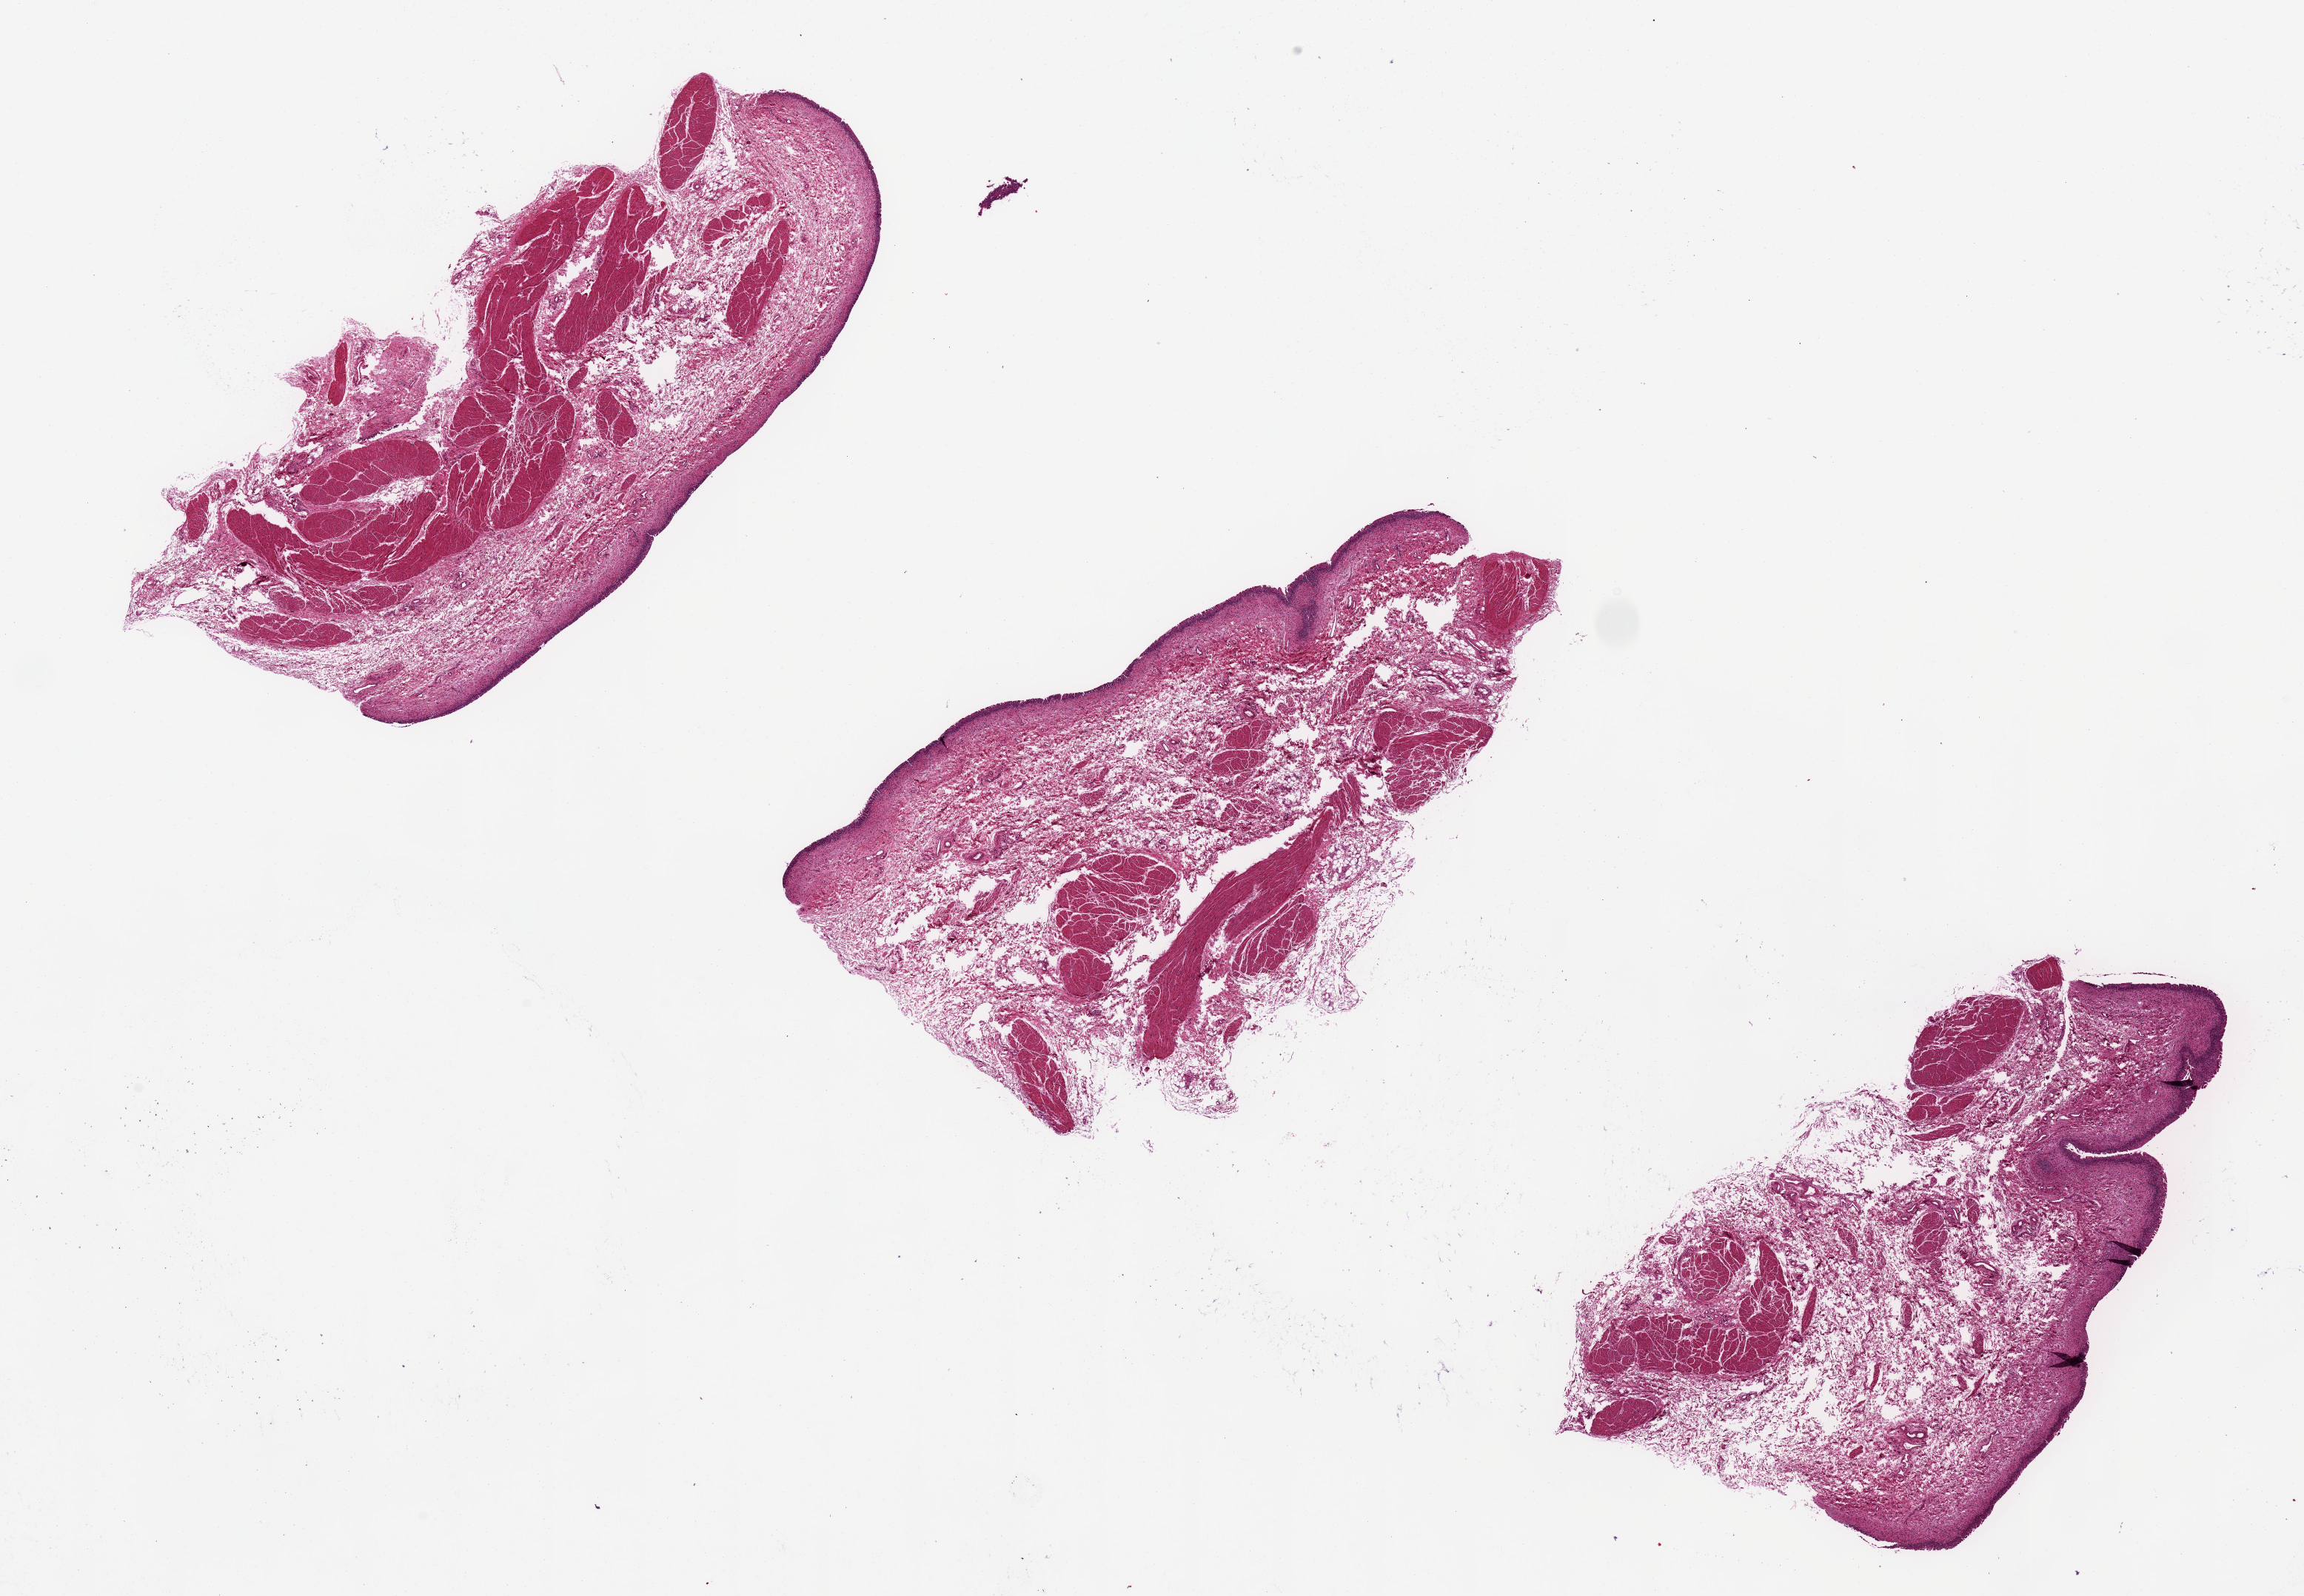
Digitized haematoxylin and eosin-stained section, brightfield, shown as a low-resolution overview of the whole scanned area (about 24.6 x 17.1 mm), PAXgene-fixed, paraffin-embedded tissue, section of urinary bladder (target tissue), tissue donor sample. Donor sex: male.
* pathologist's review note for this sample: epithelium slightly sloughed